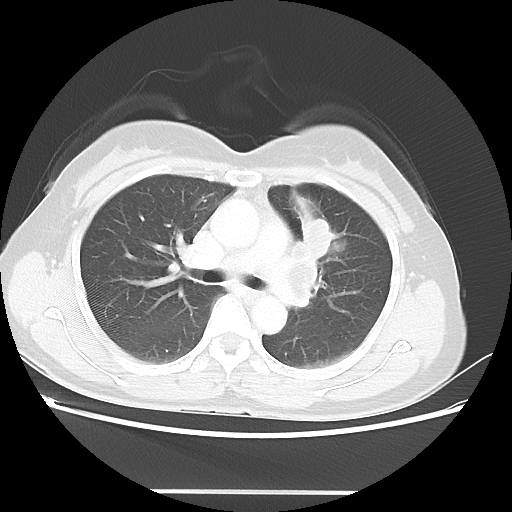
Chest CT, one axial slice. Position 29 of 46 along the scan axis. Lung window (W 1500 / L -600 HU). 5 mm slice thickness. 512 × 512 image matrix, field of view 360 × 360 mm. Female patient, age 50 years. From the clinical record (not read from this slice): clinical TNM (as recorded): T1c N1 M0; histopathological grade: G3.
Outlined on this slice (bounding box drawn by a radiologist):
- lung tumour (recorded histology: adenocarcinoma): bounding box [x1, y1, x2, y2] px = [296, 210, 333, 255]